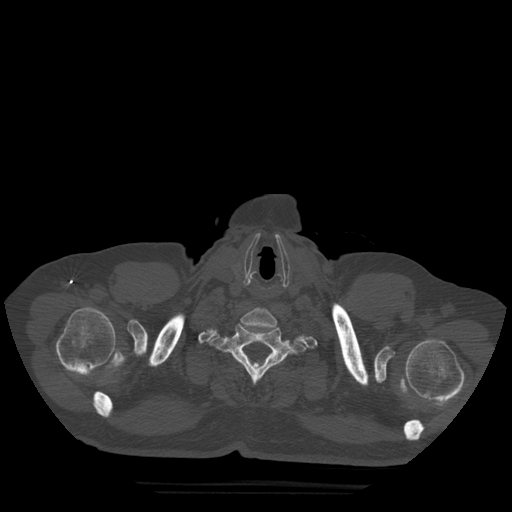
CT including the spine, one axial slice; bone window (W 1800 / L 400 HU); 1.25 mm slice thickness; 512 × 512 image matrix. Patient age 72 years. From the clinical record (not read from this slice): primary cancer: prostate.
Outlined on this slice (semi-automatically segmented with operator editing):
- T1 vertebra: bounding box [x1, y1, x2, y2] px = [209, 324, 306, 383]